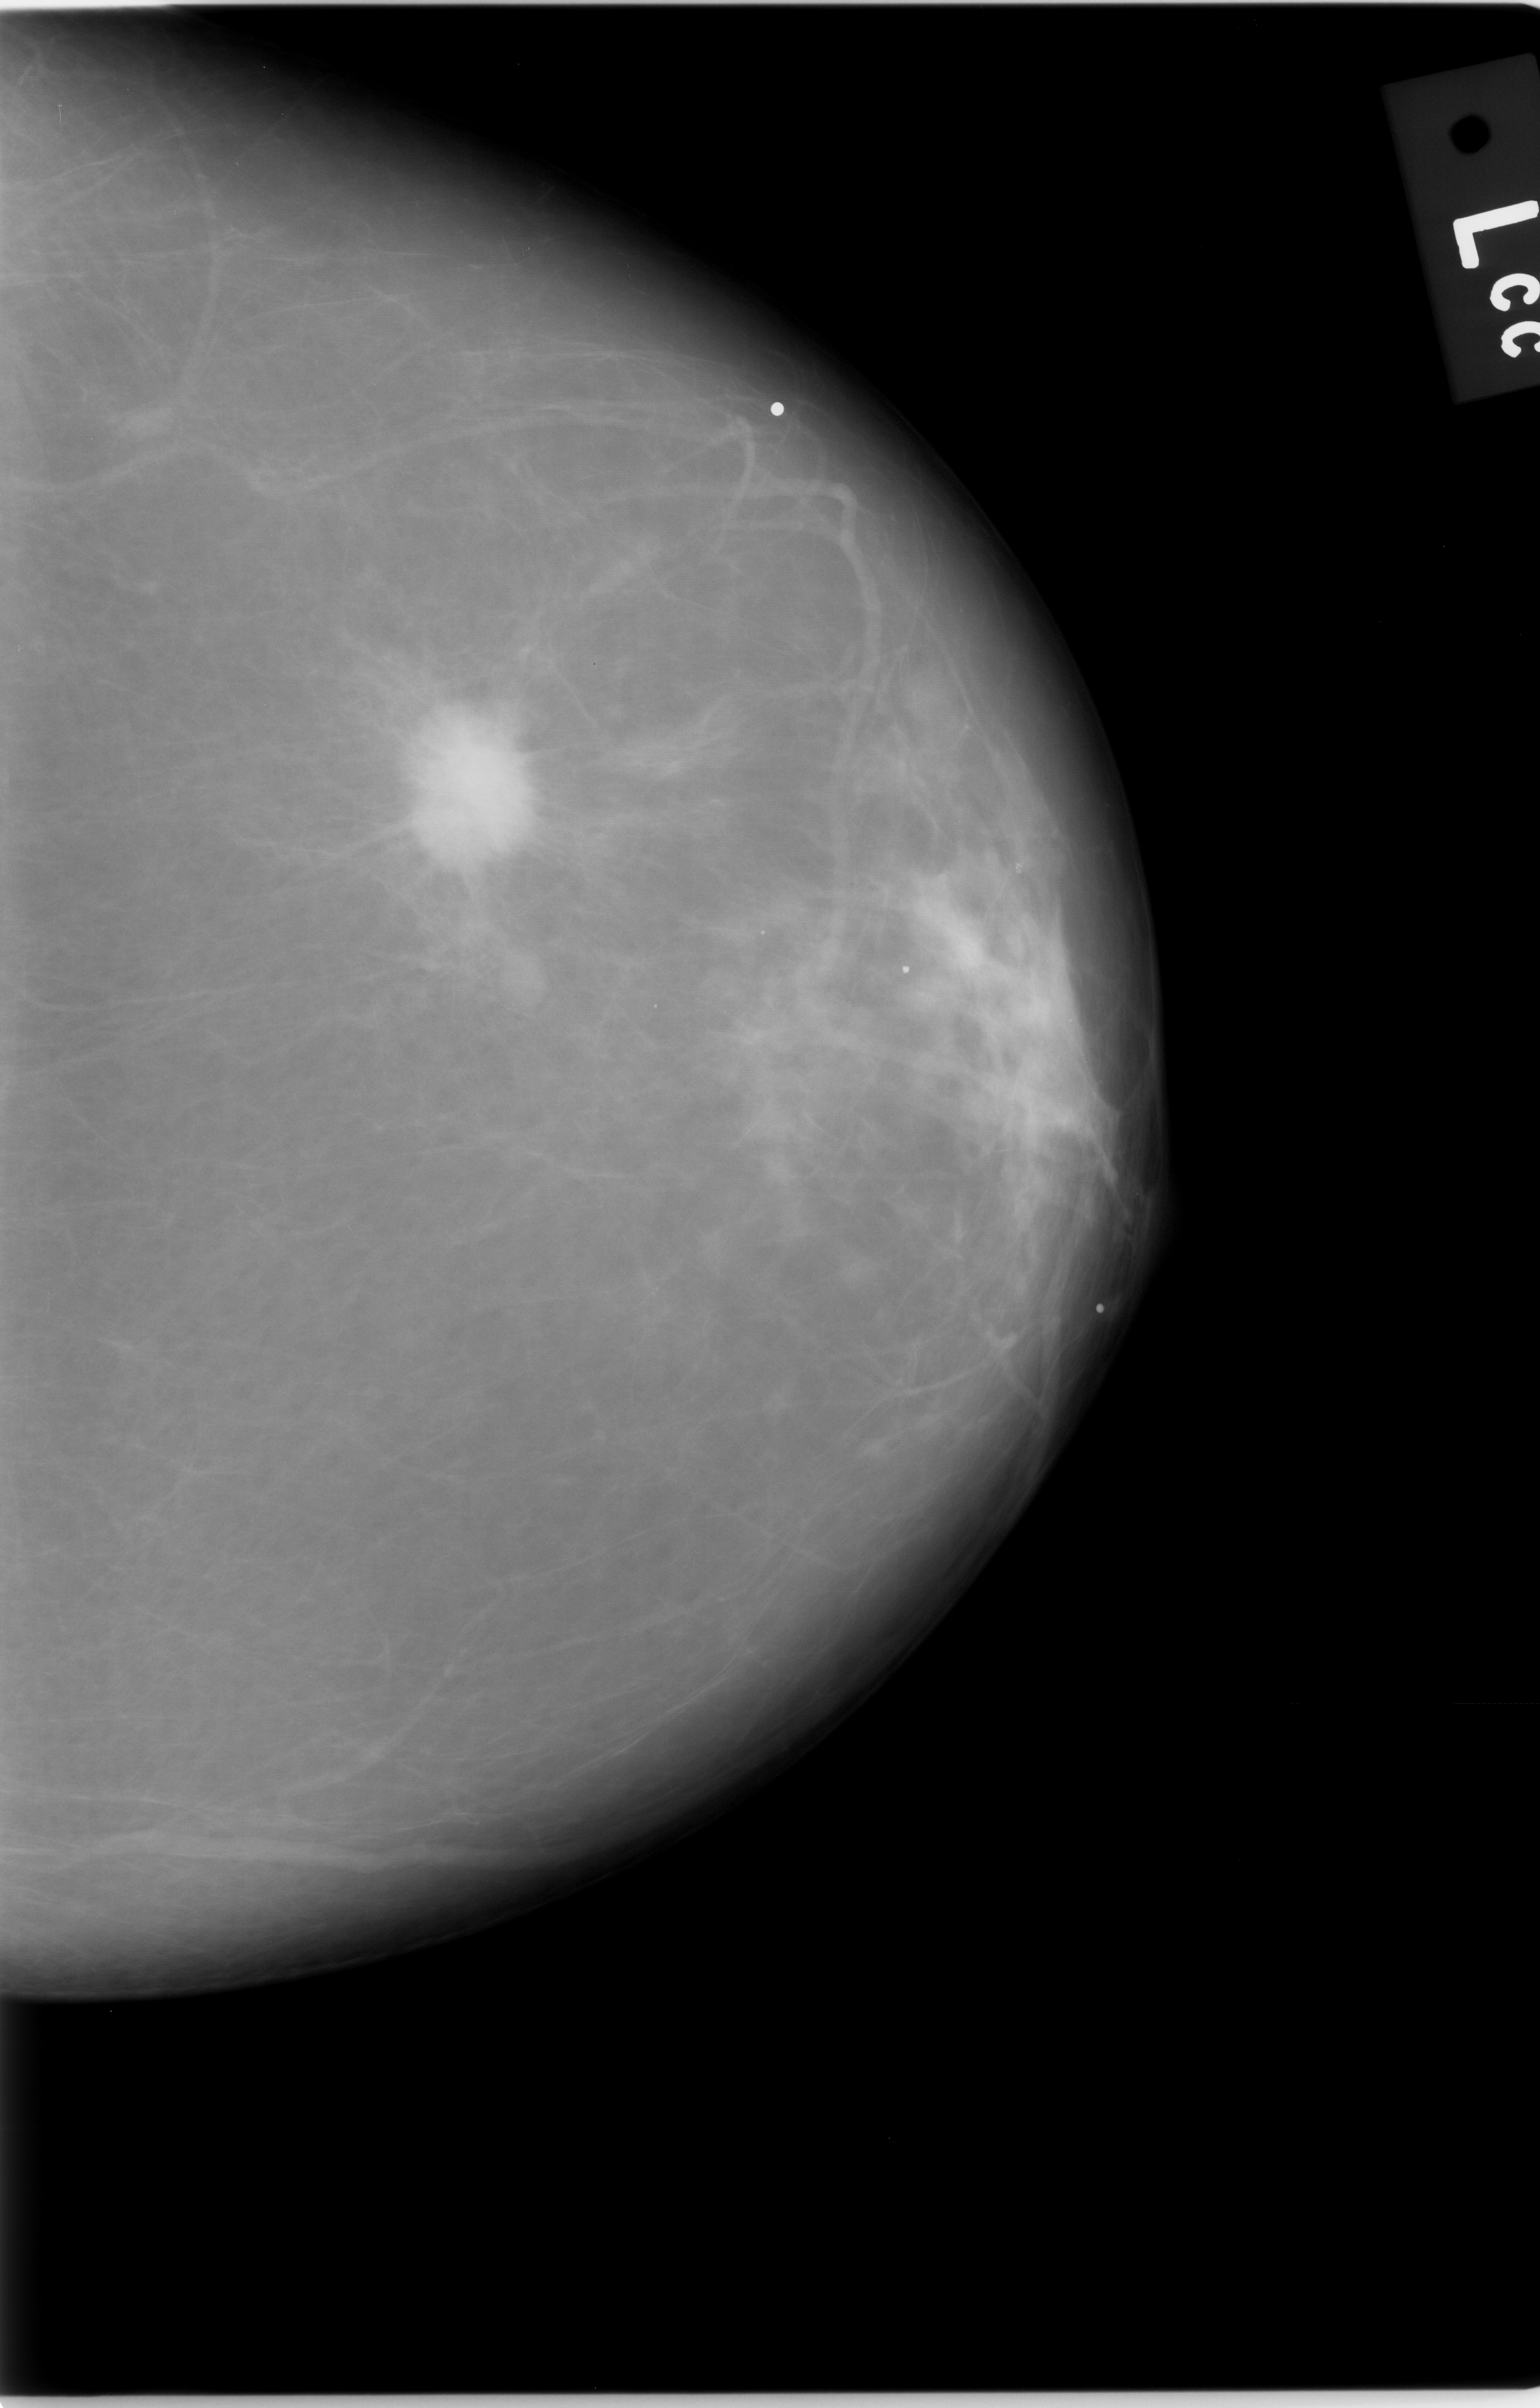
Scanned film-screen mammogram, left breast, CC view, breast composition: almost entirely fatty (BI-RADS density category 1 of 4).
- Mass, shape irregular, margins ill defined; BI-RADS assessment category 5; subtlety rating 5 on a 1 (subtle) to 5 (obvious) scale; pathology (as recorded): malignant.